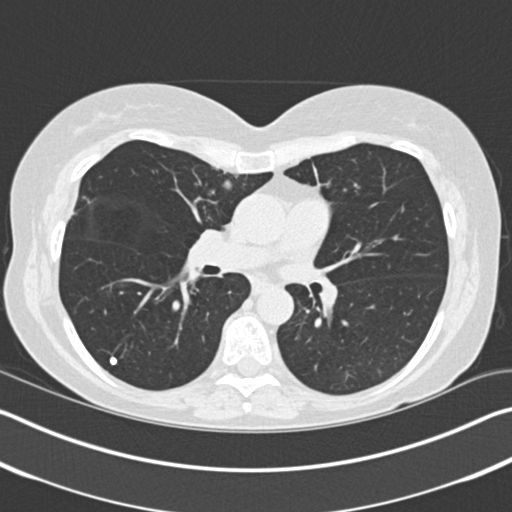
Low-dose screening chest CT, one axial slice; slice 100 of 183 in the series (ordered by position); 120 kVp; lung window (W 1500 / L -600 HU); 512 × 512 image matrix, field of view 340 × 340 mm.
Outlined on this slice (manually delineated by an expert):
- lesion 1 (tumor, upper lobe of right lung): bounding box <224,181,231,188> (left, top, right, bottom; pixels)